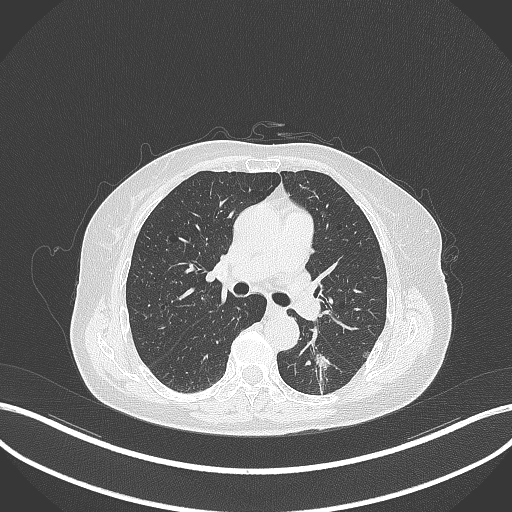
Chest CT, one axial slice. Slice 176 of 352 in the series (ordered by position). Reconstruction kernel B70f. Lung window (W 1500 / L -600 HU). 1 mm slice thickness. 512 × 512 image matrix, field of view 400 × 400 mm. Female patient, age 70 years. Case-level facts recorded for this patient, not image findings: clinical TNM (as recorded): T1c N0 M0.
Structures marked on this image (bounding box drawn by a radiologist):
- lung tumour (recorded histology: adenocarcinoma): box from (x=307, y=346) to (x=333, y=378) px